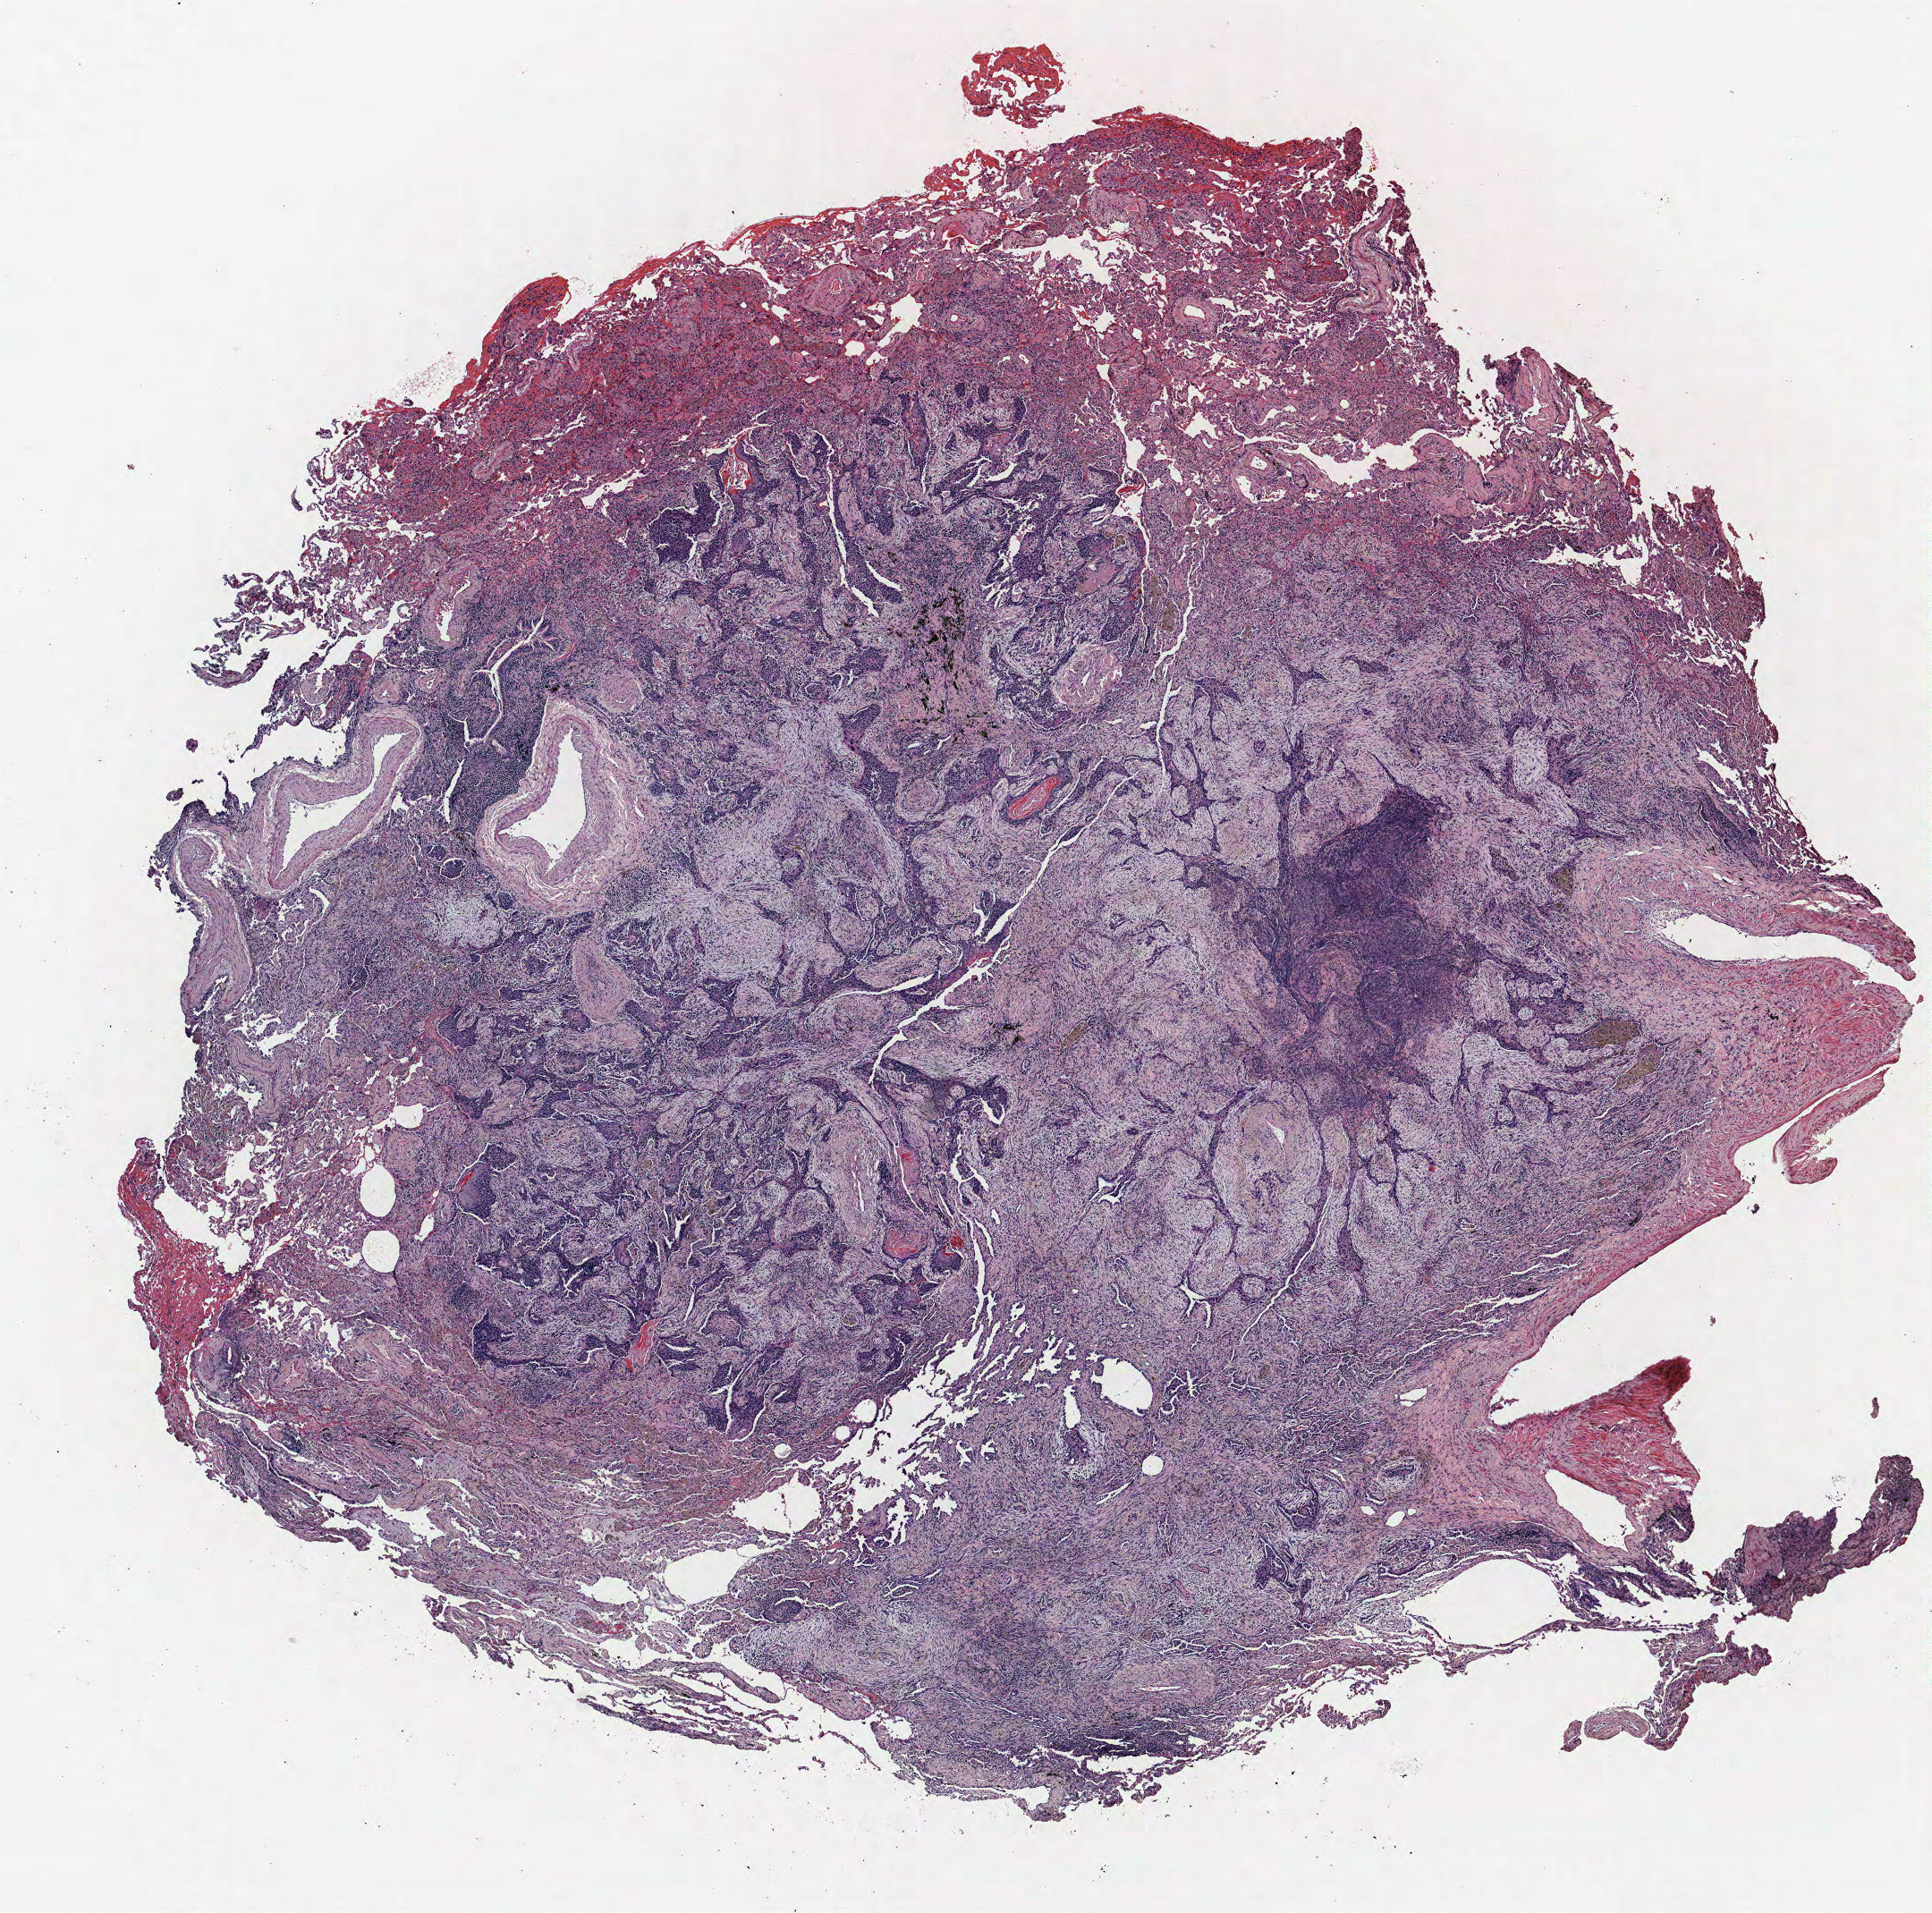
Hematoxylin and eosin (H&E) stained whole-slide image, shown as a low-resolution overview of the whole scanned area (about 8.6 x 8.6 mm, acquisition: 40x scan), FFPE section, lung. Male, age 64 at enrolment. Current smoker at enrolment. Grade: moderately differentiated (G2).
Primary tumour location (clinical record): left upper lobe. Tumour size (pathology): 10 mm. Participant's lung-cancer diagnosis: Squamous cell carcinoma, NOS (ICD-O-3 8070/3). Stage (AJCC 6th edition): IA.